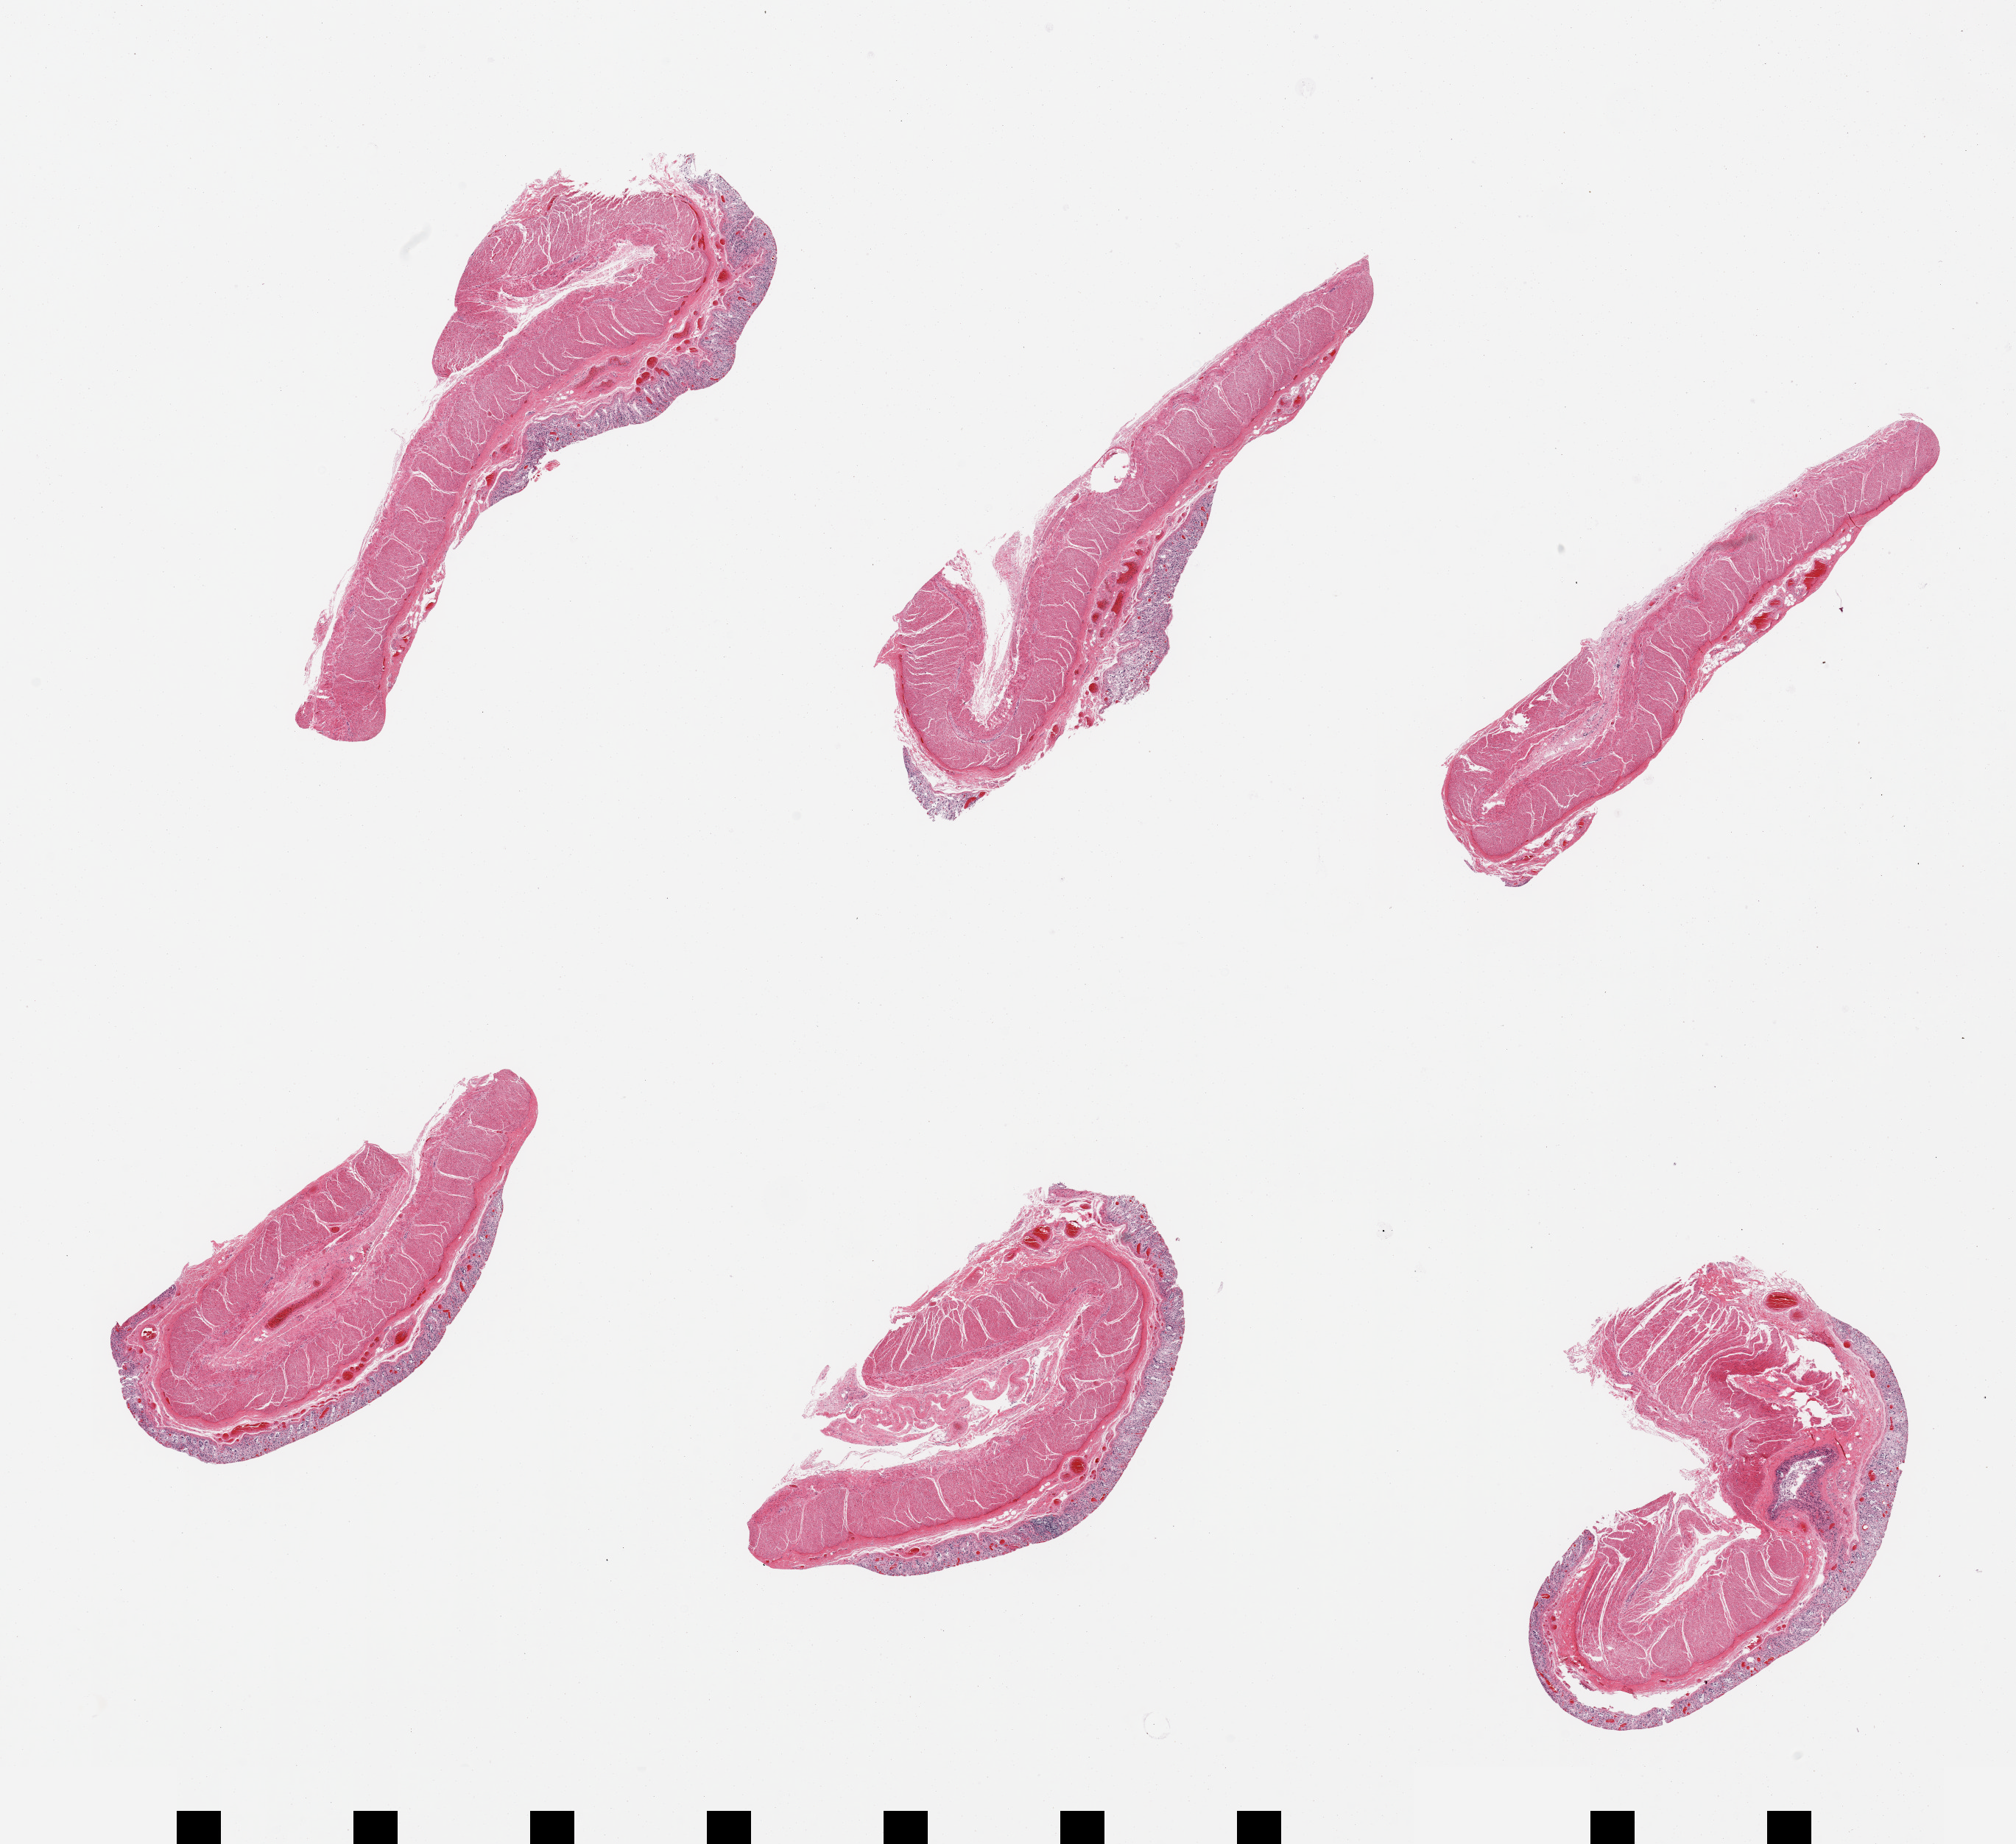
H&E whole-slide image — shown as a low-resolution overview of the whole scanned area (about 21.7 x 19.8 mm), PAXgene-fixed paraffin-embedded (PFPE) section, target tissue: transverse colon, donor tissue sample. Male donor.
- reviewer comment on this tissue sample: 6 pieces, mucosa is ~0.3 mm, ~20% thickness, glandular component completely autolyzed